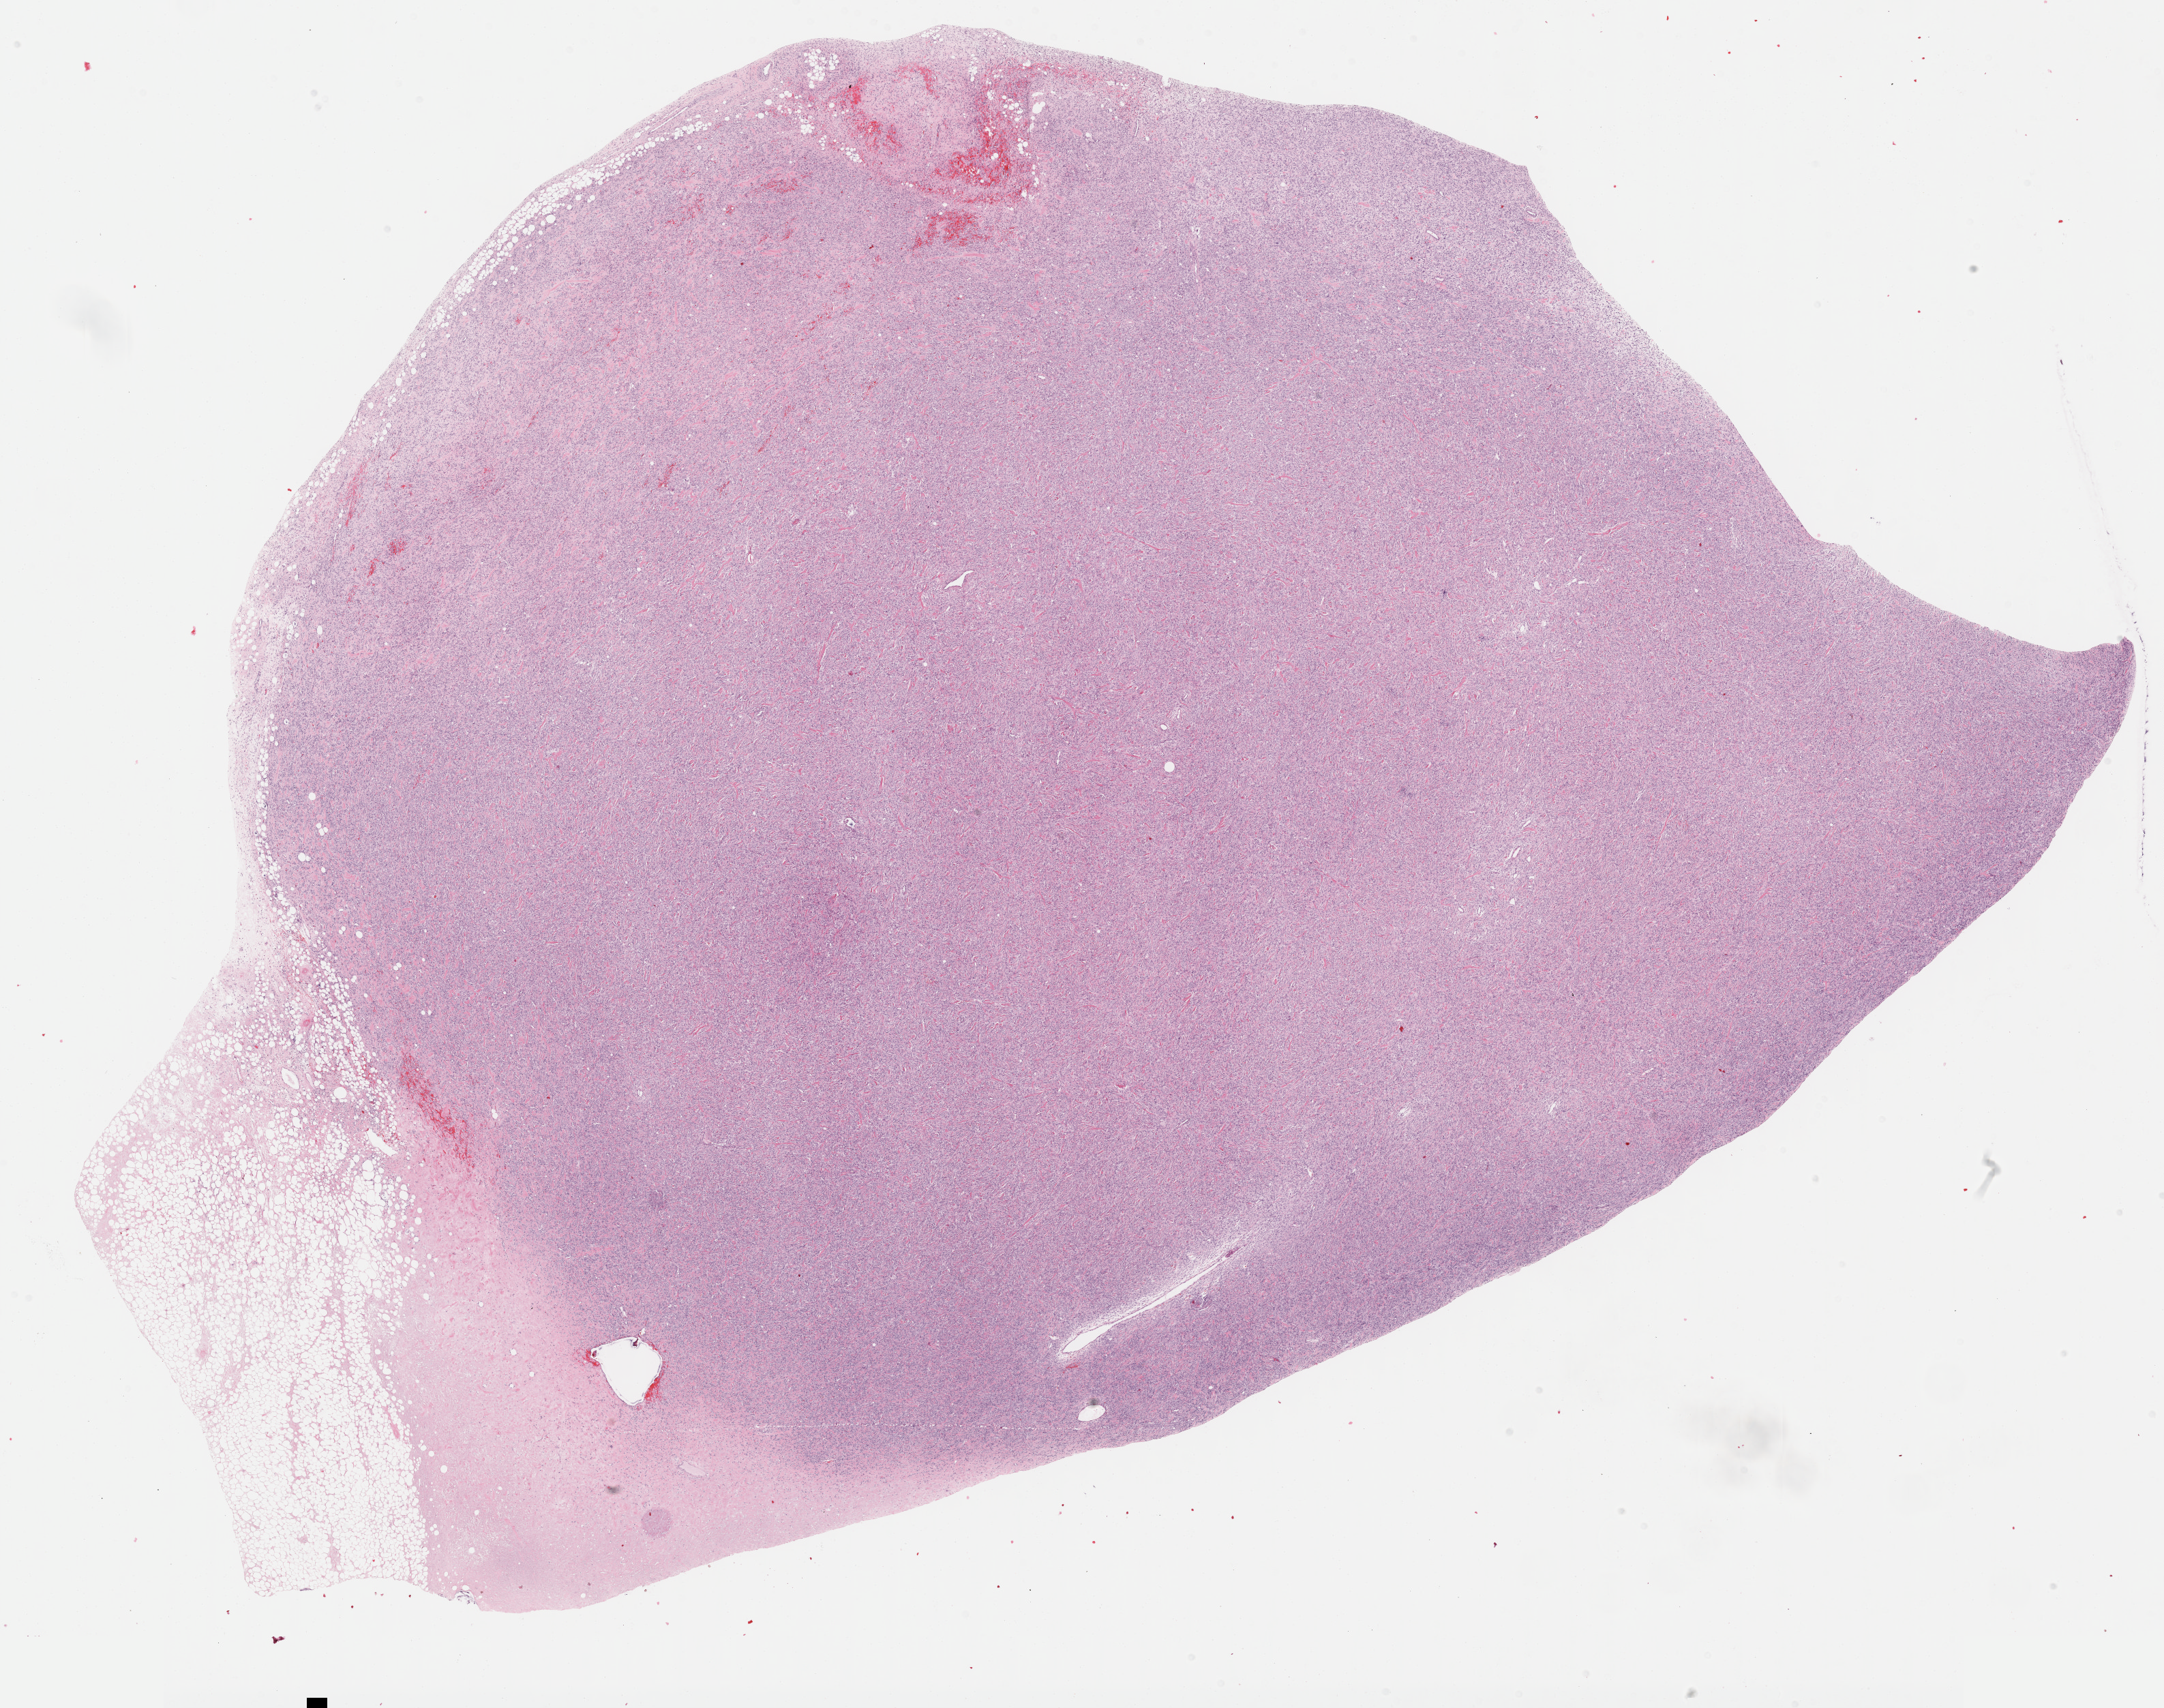
Digitized Hematoxylin and eosin (H&E) stained tissue section (whole slide) — a low-resolution overview of the entire scanned area, about 25.7 x 20.3 mm (acquisition: 40x scan); formalin-fixed paraffin-embedded (FFPE) diagnostic section; retroperitoneum and peritoneum, primary tumour sample. Male, age 67 years at initial diagnosis.
Diagnosis: Dedifferentiated liposarcoma.